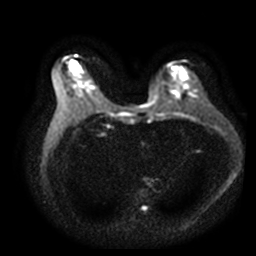
Breast MRI, one axial slice. Slice 15 of 40 in the series (ordered by position). Diffusion-weighted series; image 2 of 4 stored at this slice position (different b-values; order by instance number). 3 T. 5 mm slice thickness. 256 × 256 image matrix, field of view 360 × 360 mm. Female patient.
Annotated regions visible in this slice (expert manual segmentation):
- tumour on diffusion-weighted imaging: bounding box <70,64,75,72> (left, top, right, bottom; pixels)